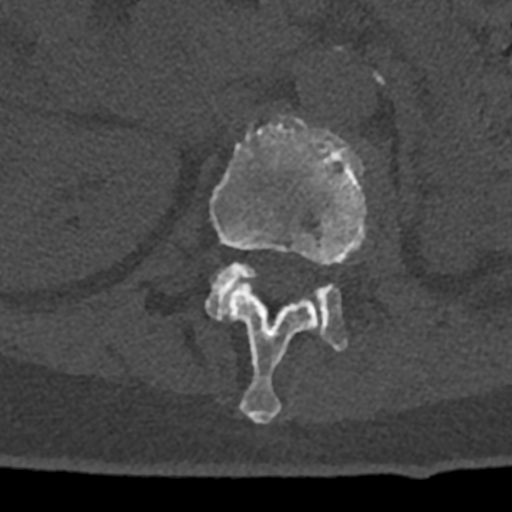
CT including the spine, one axial slice. Position 415 of 797 along the scan axis. Reconstruction kernel Br40s/3. Bone window (W 1800 / L 400 HU). 512 × 512 image matrix, field of view 160 × 160 mm. Male patient, age 74 years. Case-level facts recorded for this patient, not image findings: primary cancer: renal; vertebrae with lytic lesions (as recorded): T10, L1, L2, L3, L4, L5.
Outlined on this slice (semi-automatic segmentation, software-assisted and operator-edited):
- L1 vertebra: bounding box <210,115,368,424> (left, top, right, bottom; pixels)
- L2 vertebra: <206,261,348,352>